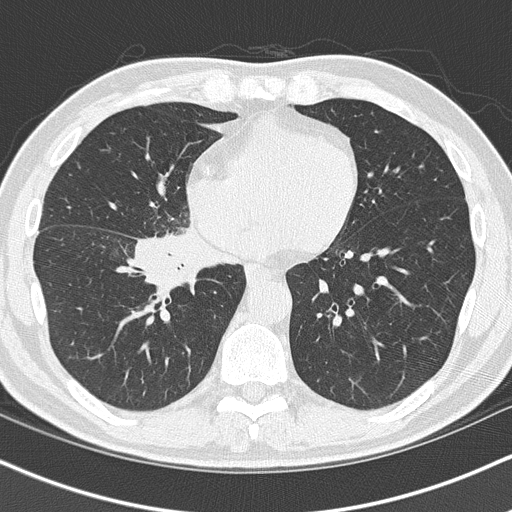
Axial slice from a low-dose chest CT screening exam, baseline screening round, lung window (W 1500 / L -600 HU), slice 50 of 151 in the series. Male, age 55 years at enrolment.
Expert-annotated lung lesion, bounding box (x1, y1, x2, y2) in pixels: (129, 225, 240, 309). The exam's reader record, not a measurement of the box and not confirmed to be the same lesion: non-calcified nodule or mass ≥4 mm, right lower lobe, 6 × 5 mm, spiculated (stellate) margins, soft tissue attenuation. Official screen result: positive, change unspecified: nodule(s) >= 4 mm or enlarging nodule(s), mass(es), or other non-specific abnormalities suspicious for lung cancer. Lung cancer was diagnosed 21 days after this screen: carcinoma, NOS, right hilum, stage IB (AJCC 6th edition), 67 mm at pathology.